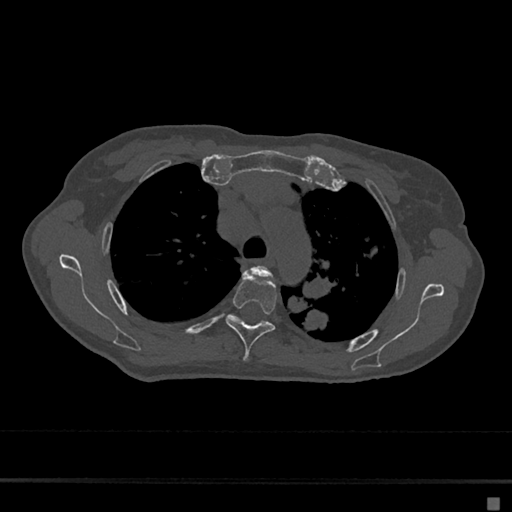
CT including the spine, one axial slice. Position 498 of 797 along the scan axis. Reconstruction kernel Br40s/3. 120 kVp. Bone window (W 1800 / L 400 HU). 0.5 mm slice thickness. 512 × 512 image matrix, field of view 360 × 360 mm. Female patient, age 68 years. Case-level facts recorded for this patient, not image findings: primary cancer: renal.
Structures marked on this image (semi-automatically segmented with operator editing):
- T3 vertebra: bounding box [x1, y1, x2, y2] px = [253, 266, 271, 276]
- T4 vertebra: [225, 274, 277, 362]
- T5 vertebra: [230, 315, 258, 325]